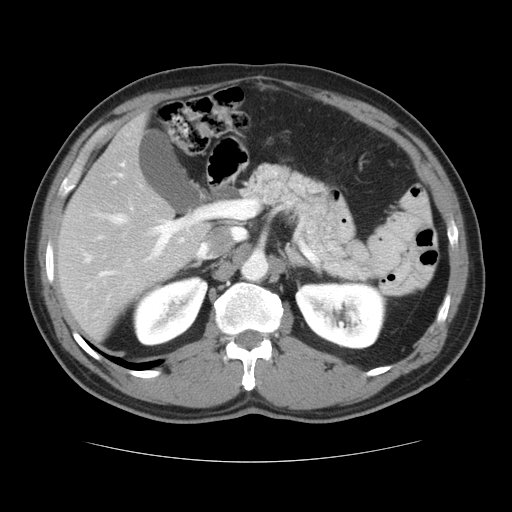
Contrast-enhanced abdominal CT, one axial slice; position 20 of 37 along the scan axis; soft-tissue window (W 400 / L 40 HU); 5 mm slice thickness; 512 × 512 image matrix, field of view 374 × 374 mm. Male patient, age 66 years. From the clinical record (not read from this slice): diagnosis: colorectal cancer liver metastases, imaged before liver resection; multiple liver metastases: yes; largest metastasis: 1.6 cm.
Annotated regions visible in this slice (expert manual segmentation):
- hepatic veins: box from (x=97, y=173) to (x=210, y=258) px
- liver: (x=59, y=116)–(x=211, y=341)
- planned liver remnant (the part of the liver to remain after resection): (x=59, y=202)–(x=211, y=341)
- portal vein (with intrahepatic branches): (x=99, y=162)–(x=214, y=277)